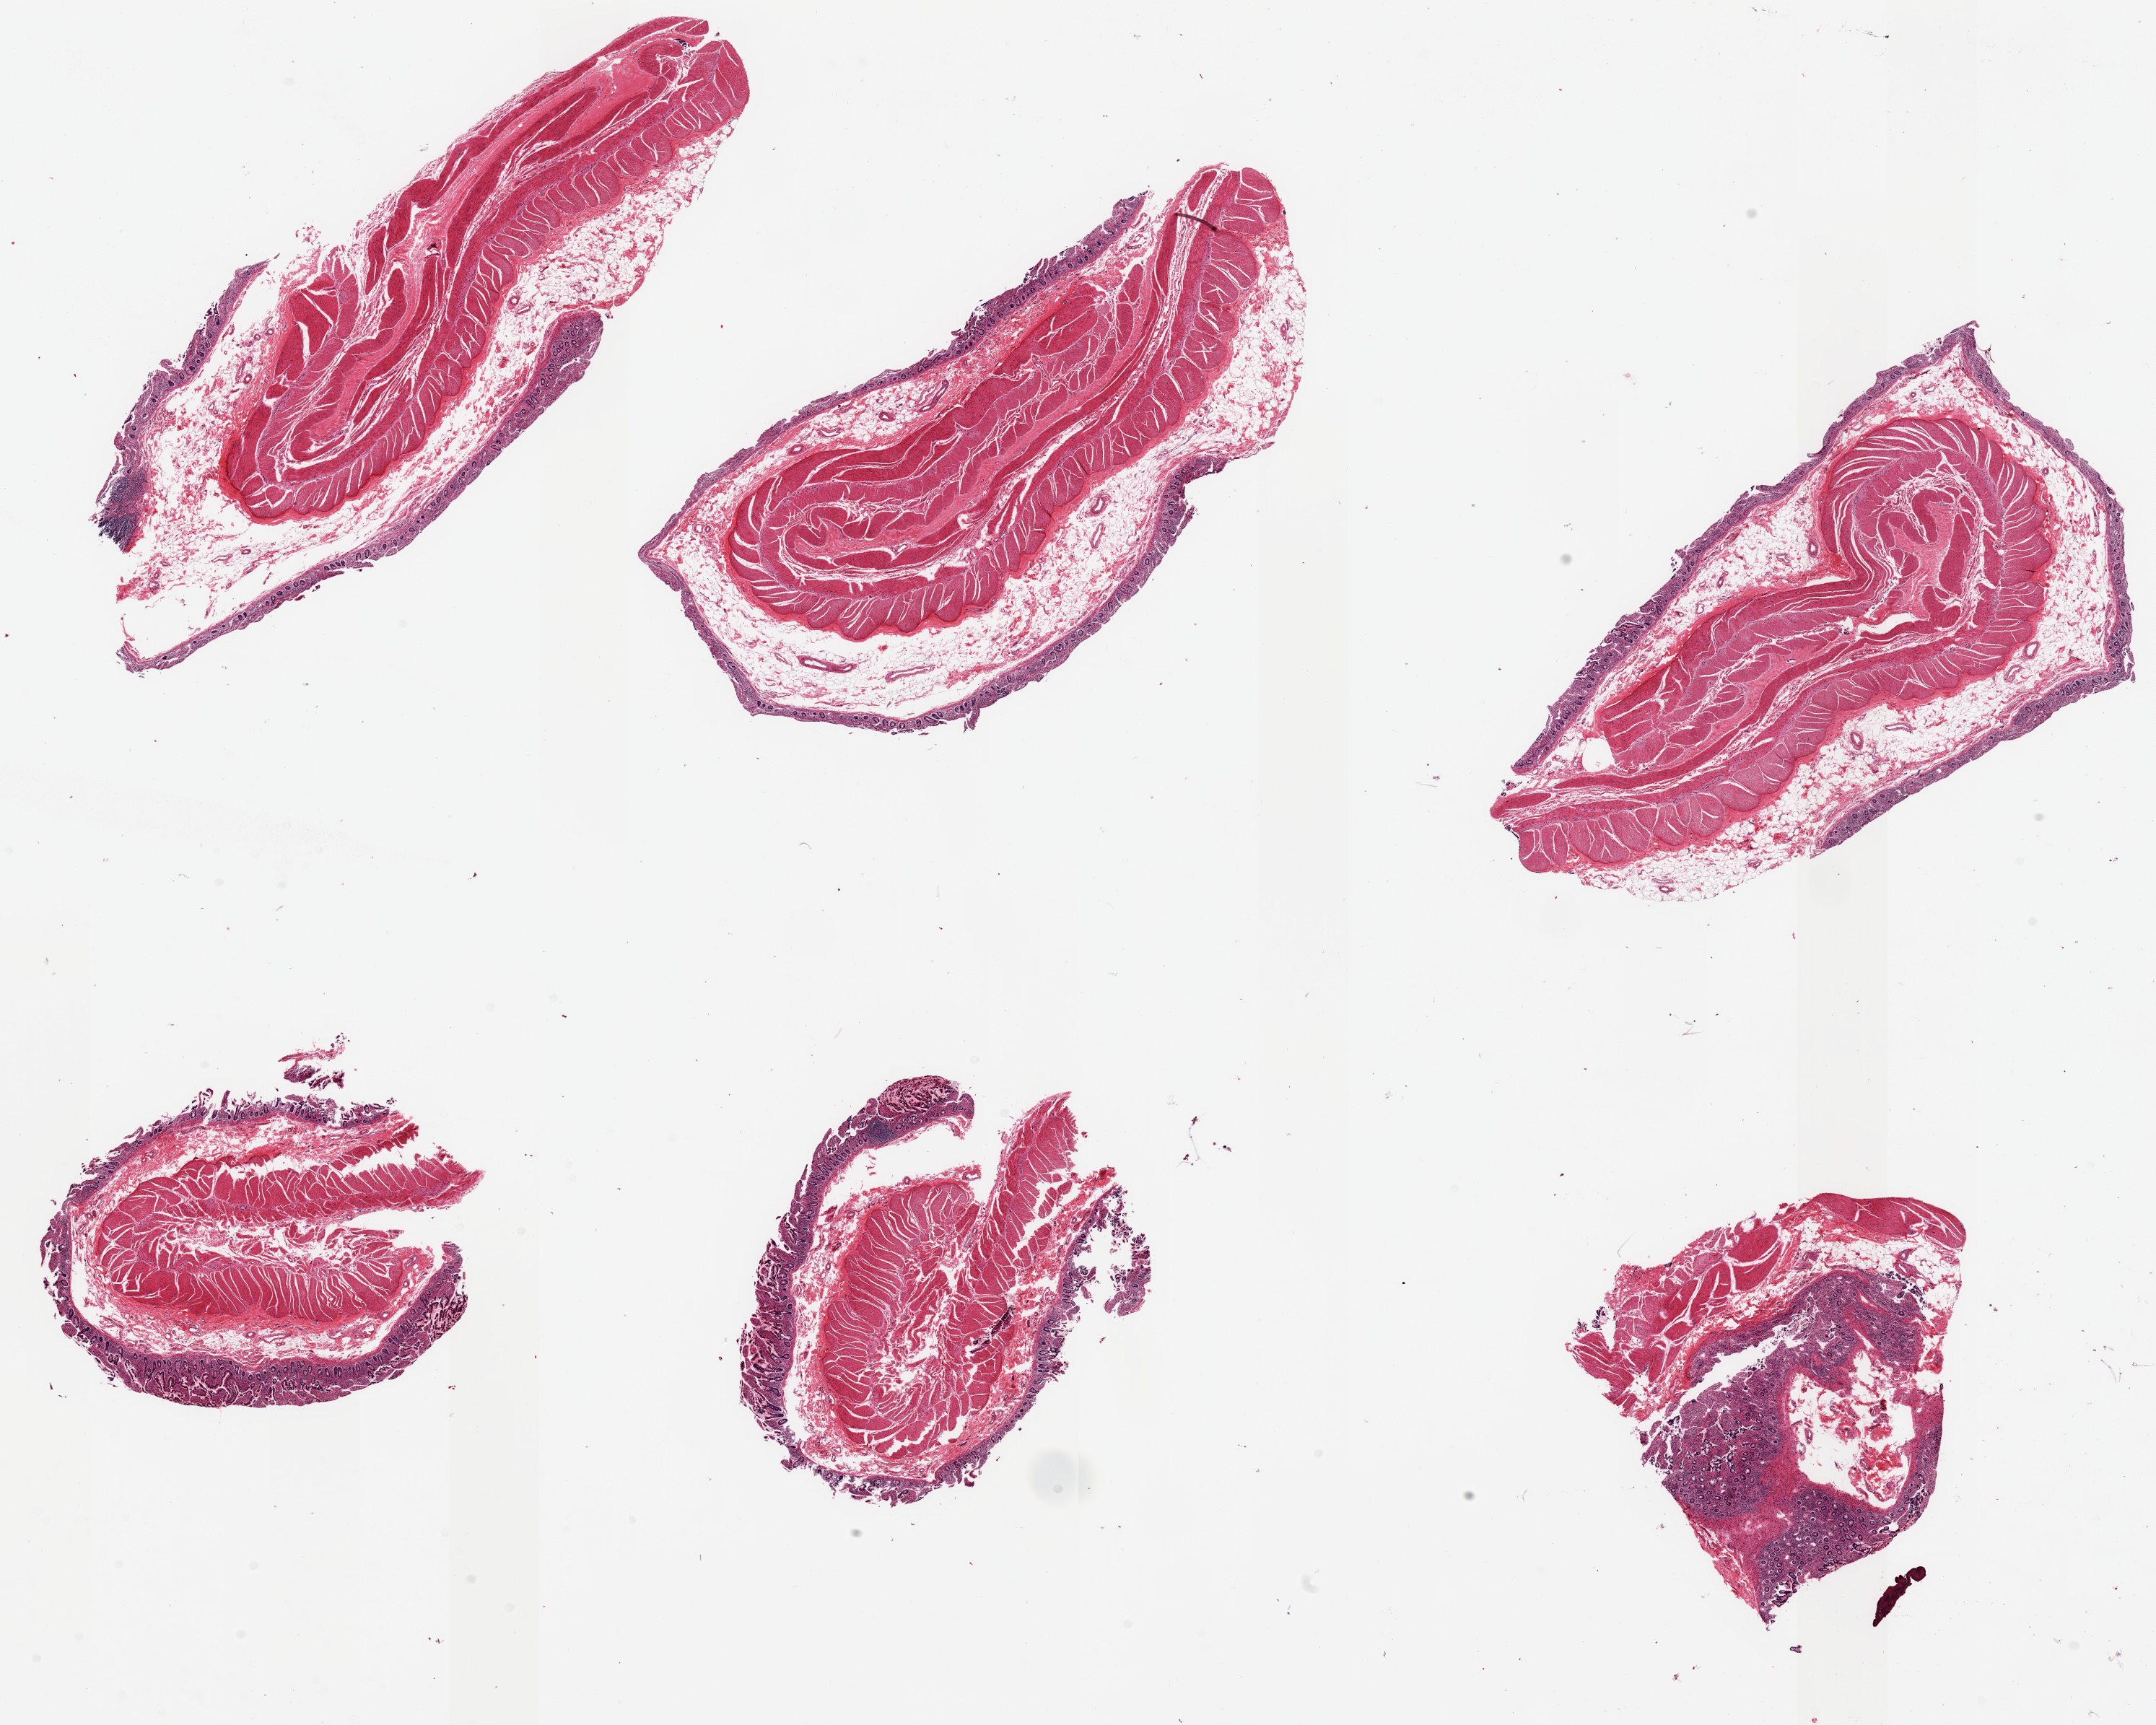
H&E whole-slide image — shown as a low-resolution overview of the whole scanned area (about 23.6 x 18.9 mm), PAXgene-fixed paraffin-embedded (PFPE) section, target tissue: ileum, donor tissue sample. Donor: male.
Reviewer comment on this tissue sample: 6 pieces, only trace target lymphoid aggregates.